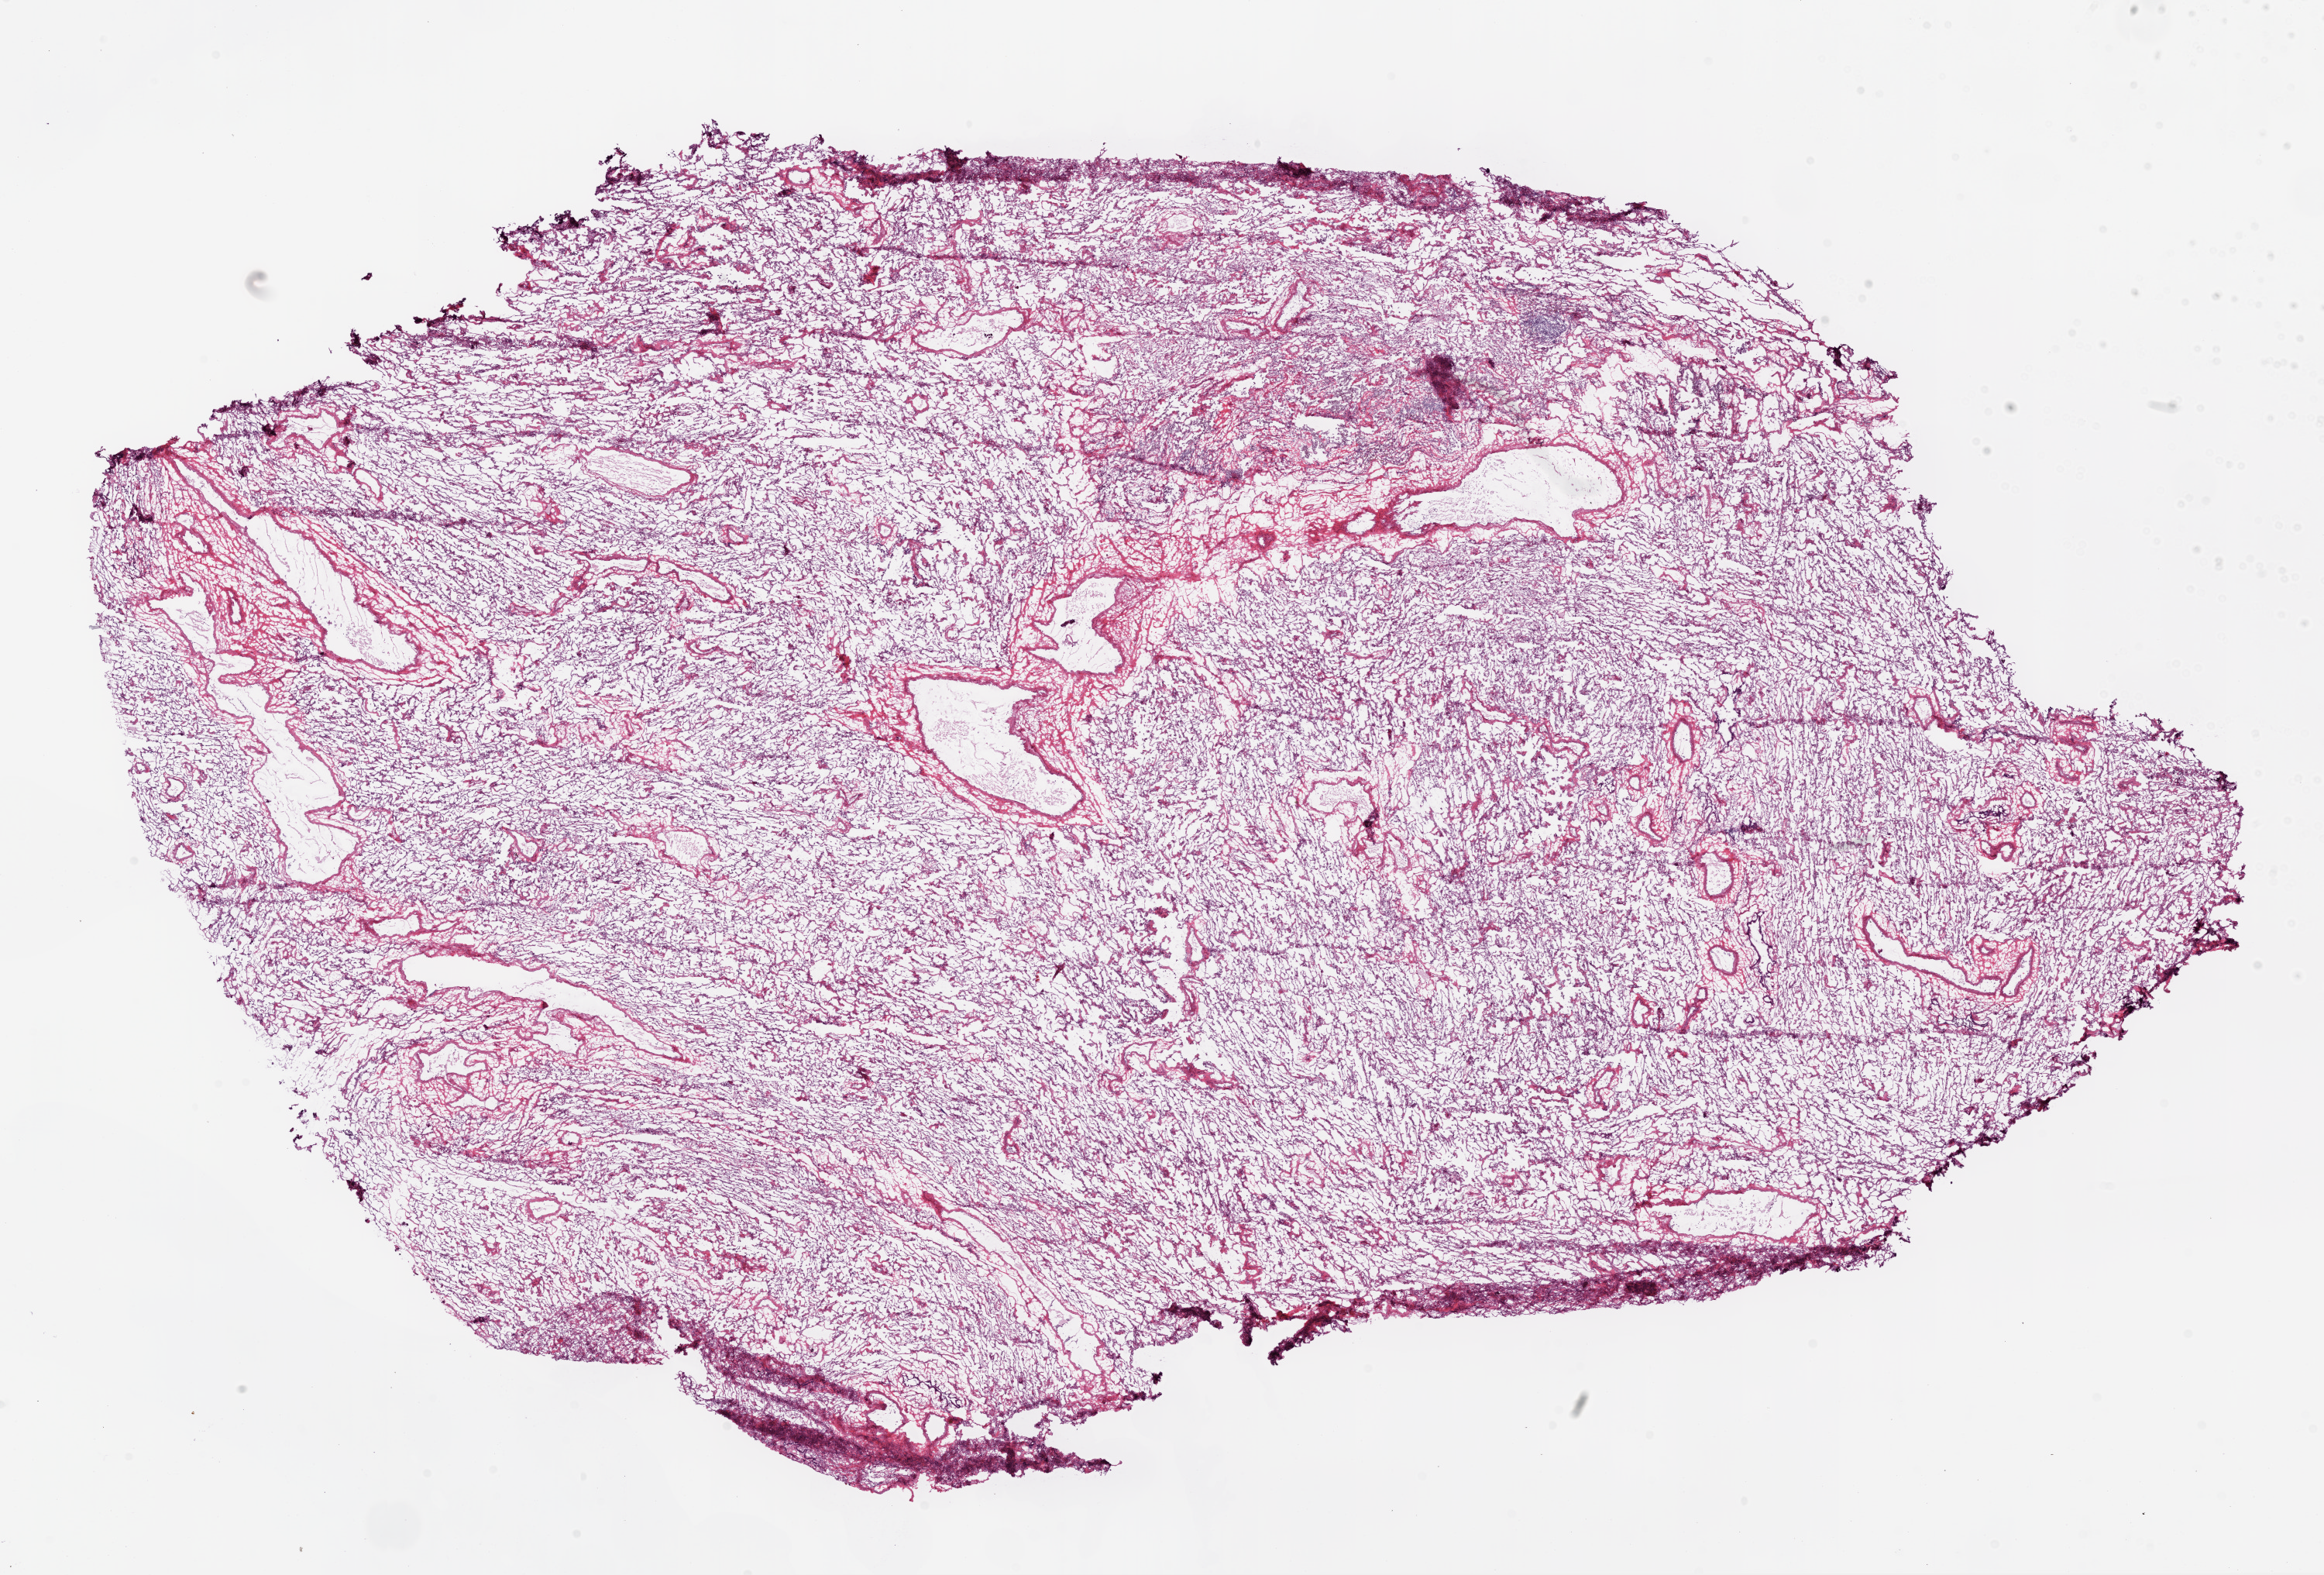
H&E-stained whole-slide image — whole scanned area (about 24.1 x 16.3 mm, slide scanned at 20x) shown as a low-resolution overview; frozen section from the bottom of the tissue portion; lung, solid tissue normal (non-tumour tissue) sample. Patient: male, age at initial diagnosis 73 years.
- this section: solid tissue normal (non-tumour) sample from the same patient
- patient diagnosis: Squamous cell carcinoma, NOS (upper lobe, lung)